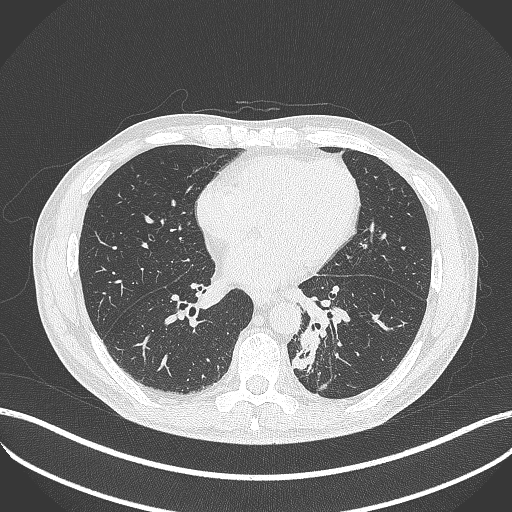
Chest CT, one axial slice; slice 166 of 451 in the series (ordered by position); lung window (W 1500 / L -600 HU); 512 × 512 image matrix. Patient: male, 72 years. Case-level facts recorded for this patient, not image findings: clinical TNM (as recorded): T2b N0 M1.
Annotated regions visible in this slice (bounding box drawn by a radiologist):
- lung tumour (recorded histology: adenocarcinoma): bounding box <292,319,324,376> (left, top, right, bottom; pixels)